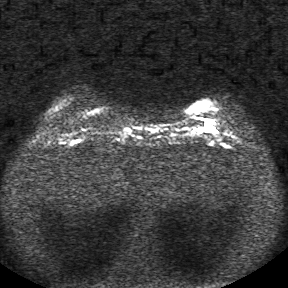
Breast MRI, one axial slice. Slice 6 of 34 in the series (ordered by position). Diffusion-weighted series; image 2 of 4 stored at this slice position (different b-values; order by instance number). 1.5 T. 5 mm slice thickness. 288 × 288 image matrix. Female patient.
Outlined on this slice (expert manual segmentation):
- tumour on diffusion-weighted imaging: bounding box [x1, y1, x2, y2] px = [202, 126, 215, 131]